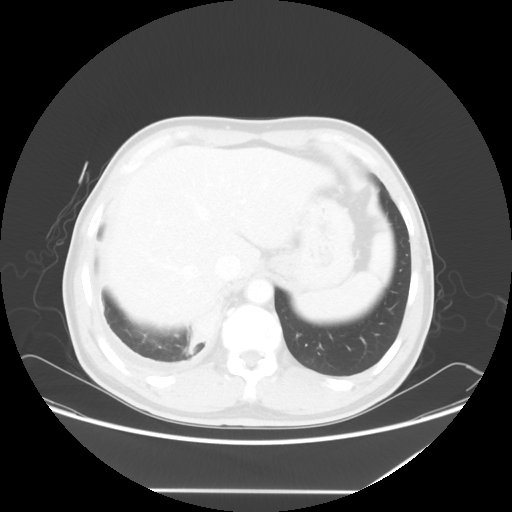
Chest CT, one axial slice; position 10 of 60 along the scan axis; reconstruction kernel STANDARD; 120 kVp; lung window (W 1500 / L -600 HU); 5 mm slice thickness; 512 × 512 image matrix, field of view 419 × 419 mm. Patient: male, 48 years. From the clinical record (not read from this slice): clinical TNM (as recorded): T3 N3 M1a.
Structures marked on this image (bounding box drawn by a radiologist):
- lung tumour (recorded histology: squamous cell carcinoma): bounding box [x1, y1, x2, y2] px = [183, 296, 226, 363]